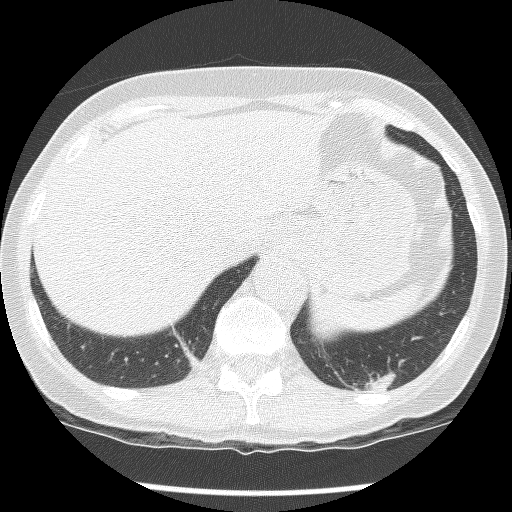
Axial slice from a low-dose chest CT screening exam; second screening round (one year after baseline); lung window (W 1500 / L -600 HU); 2.5 mm slice thickness; slice 109 of 136 in the series. Female, age 61 years at enrolment.
Expert-annotated lung lesion, bounding box <325,304,442,411> (left, top, right, bottom; pixels). The screening reader recorded 2 non-calcified nodules or masses ≥4 mm on this exam (left lower lobe, left lower lobe); which of them this box marks is not recorded. Lung cancer was diagnosed 585 days after this screen (after the third annual screen): non-small cell carcinoma, left lower lobe, poorly differentiated (G3), stage IB (AJCC 6th edition), 100 mm at pathology.